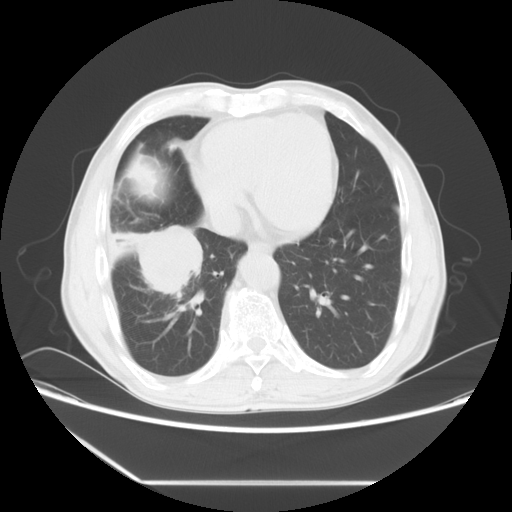
Chest CT, one axial slice. Position 21 of 60 along the scan axis. Lung window (W 1500 / L -600 HU). 512 × 512 image matrix, field of view 386 × 386 mm. Male patient, age 72 years. From the clinical record (not read from this slice): clinical TNM (as recorded): T1c N0 M0.
Structures marked on this image (bounding box drawn by a radiologist):
- lung tumour (recorded histology: squamous cell carcinoma): bounding box [x1, y1, x2, y2] px = [110, 221, 212, 309]